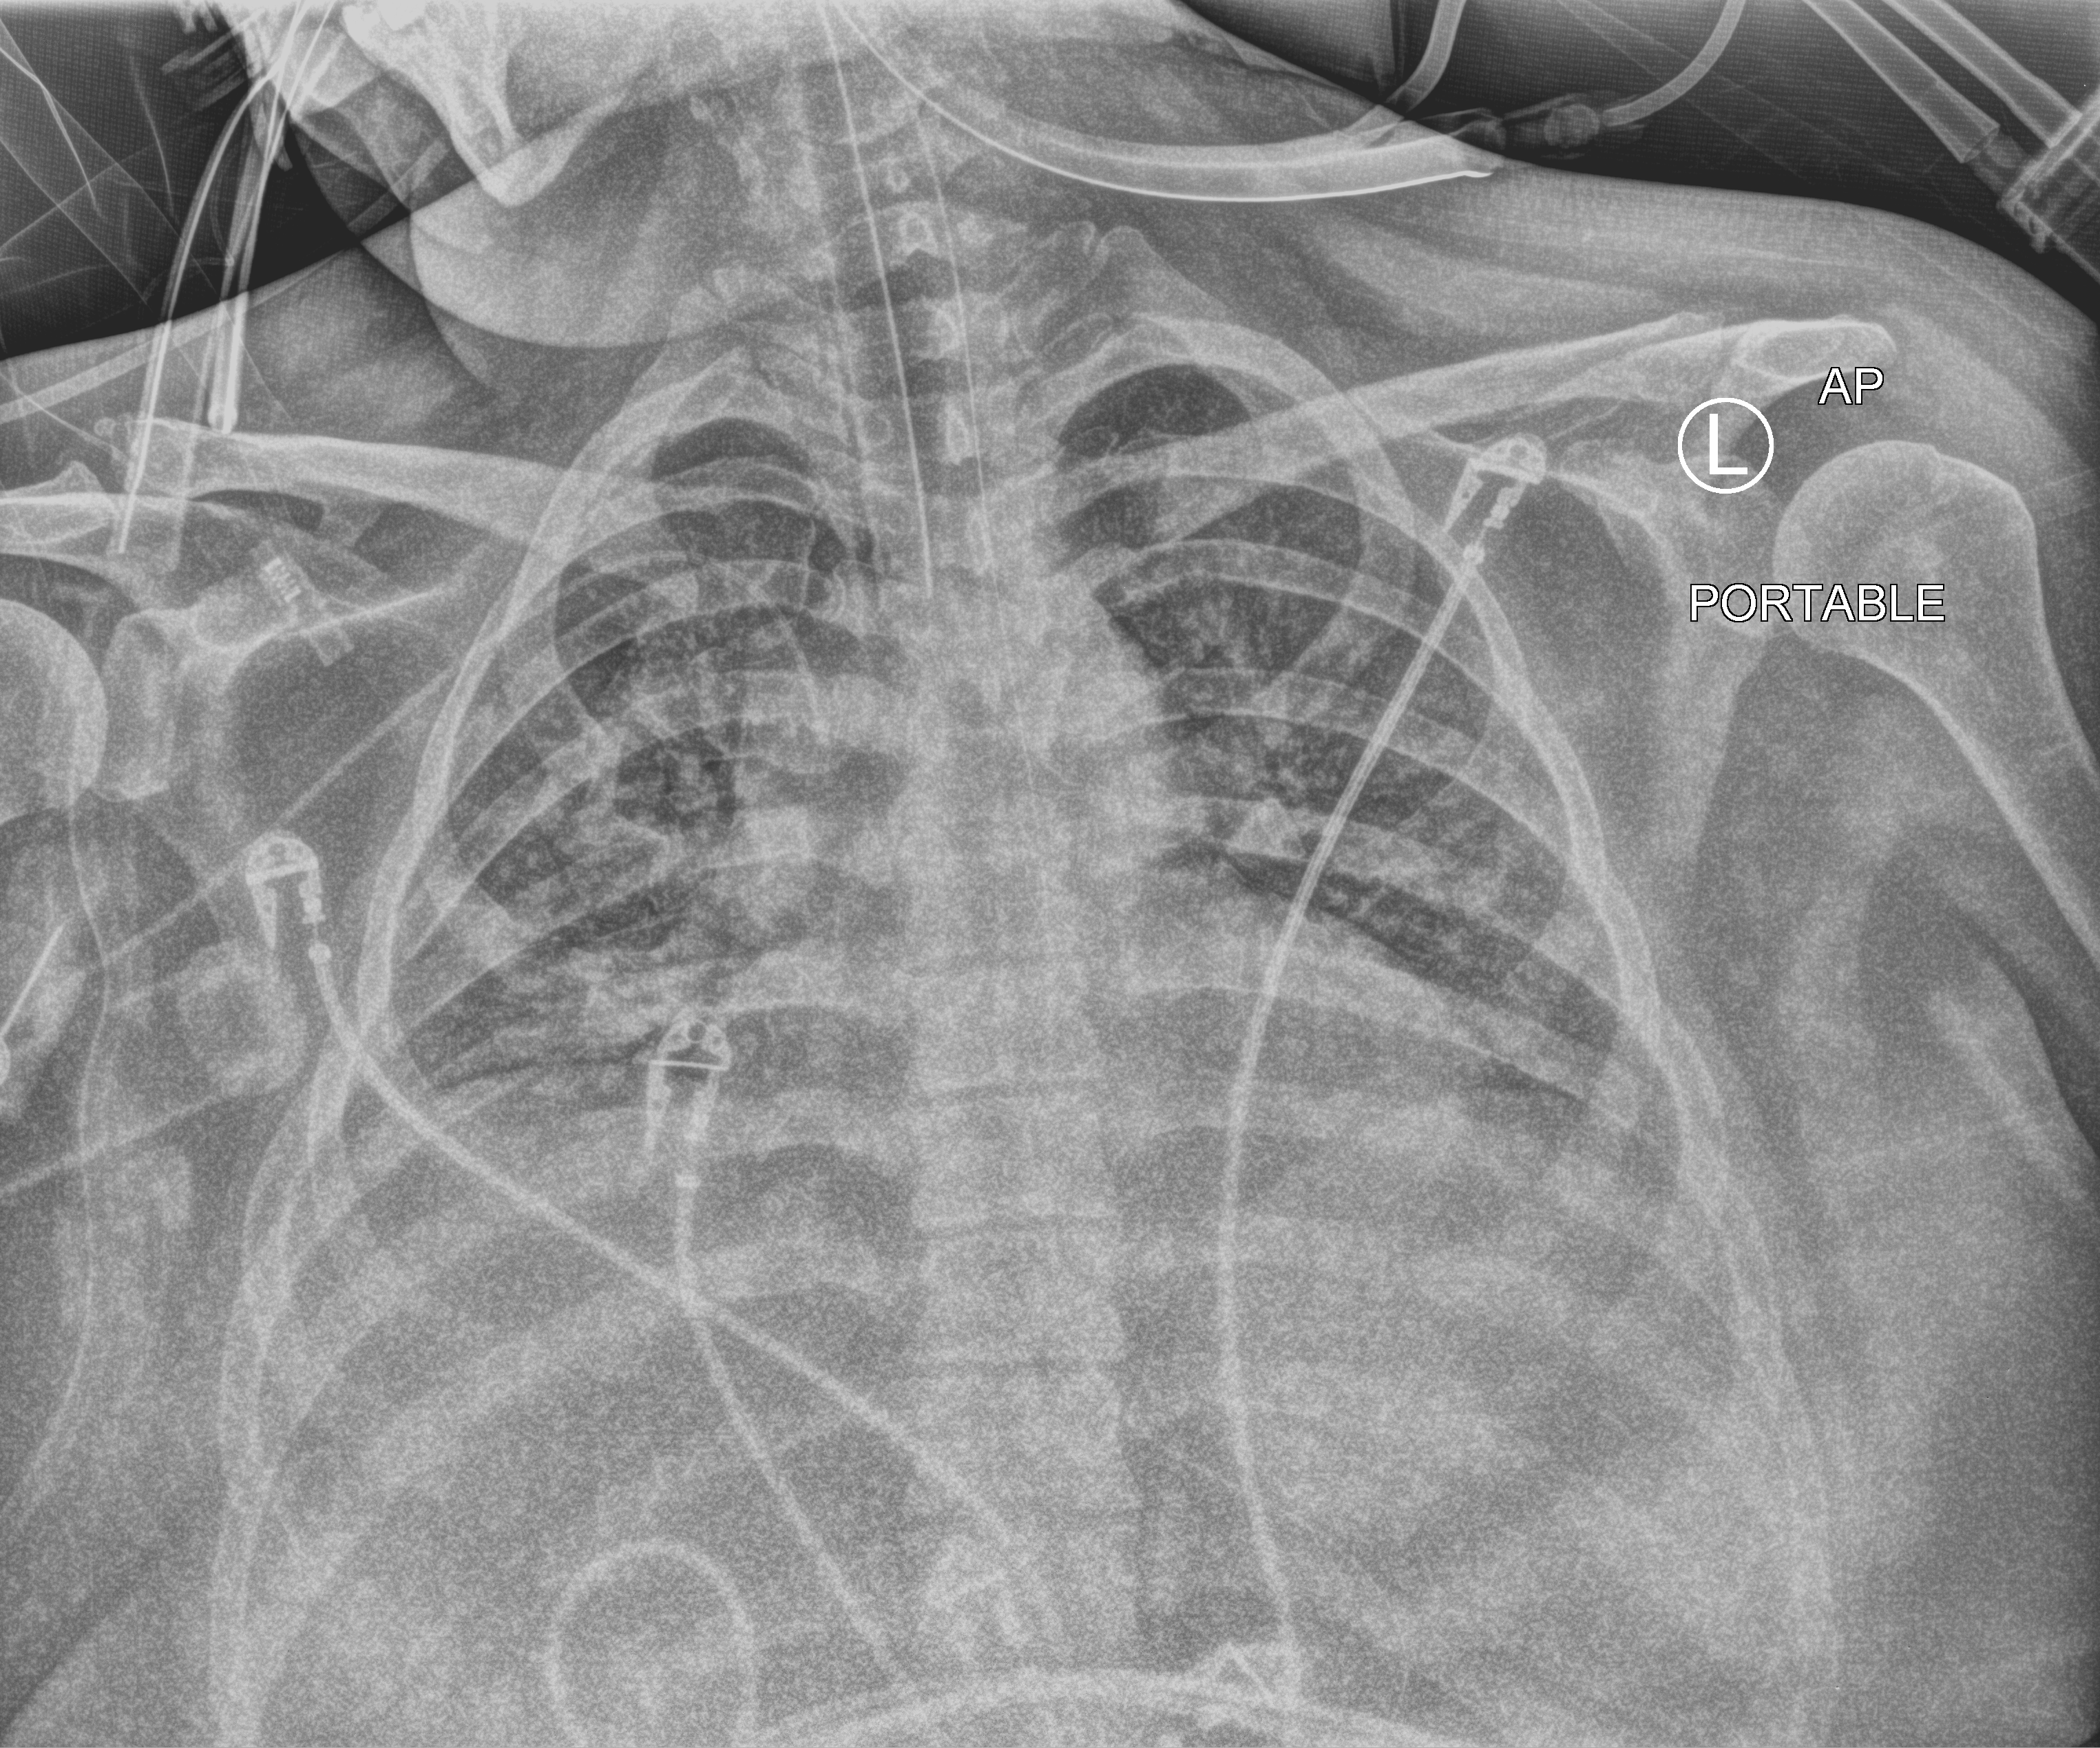
Portable chest radiograph; anteroposterior (AP) projection. Patient hospitalised with COVID-19; female, aged 18–59 years.
Hospital-stay facts (about this admission, not read from this image; timing relative to this image not recorded): mechanically ventilated during this hospital stay: yes; length of hospital stay: 25 days.